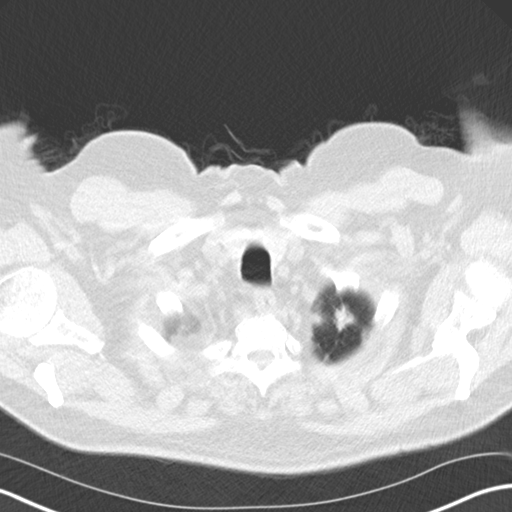
Chest CT (low-dose screening protocol), one axial image; third screening round (two years after baseline); lung window (W 1500 / L -600 HU); 5 mm slice thickness; slice 7 of 69 in the series. Male participant, aged 67 years at enrolment. Former smoker at enrolment.
- Expert reader's lesion annotation, bounding box <325,297,361,337> (left, top, right, bottom; pixels).
- Screening reader's record for this exam (one nodule recorded; not confirmed to be the boxed lesion): non-calcified nodule or mass ≥4 mm, left upper lobe, 20 × 15 mm, spiculated (stellate) margins, soft tissue attenuation, pre-existing on the prior screen: yes; interval growth: yes.
- Official screen result: positive, other.
- Lung cancer was diagnosed 52 days after this screen: adenocarcinoma, NOS, left upper lobe, moderately differentiated (G2), stage IIA (AJCC 6th edition), 18 mm at pathology.